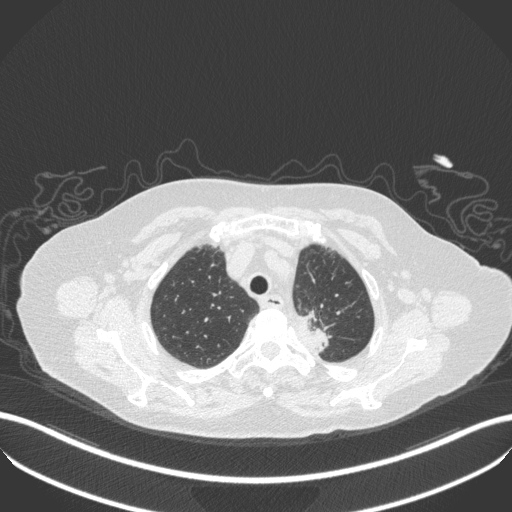
Chest CT, one axial slice; slice 281 of 353 in the series (ordered by position); reconstruction kernel B31f; lung window (W 1500 / L -600 HU); 1 mm slice thickness; 512 × 512 image matrix, field of view 400 × 400 mm. Female patient, age 81 years. Case-level facts recorded for this patient, not image findings: clinical TNM (as recorded): T2a N0 M0.
Structures marked on this image (bounding box drawn by a radiologist):
- lung tumour (recorded histology: adenocarcinoma): bounding box [x1, y1, x2, y2] px = [287, 303, 332, 356]